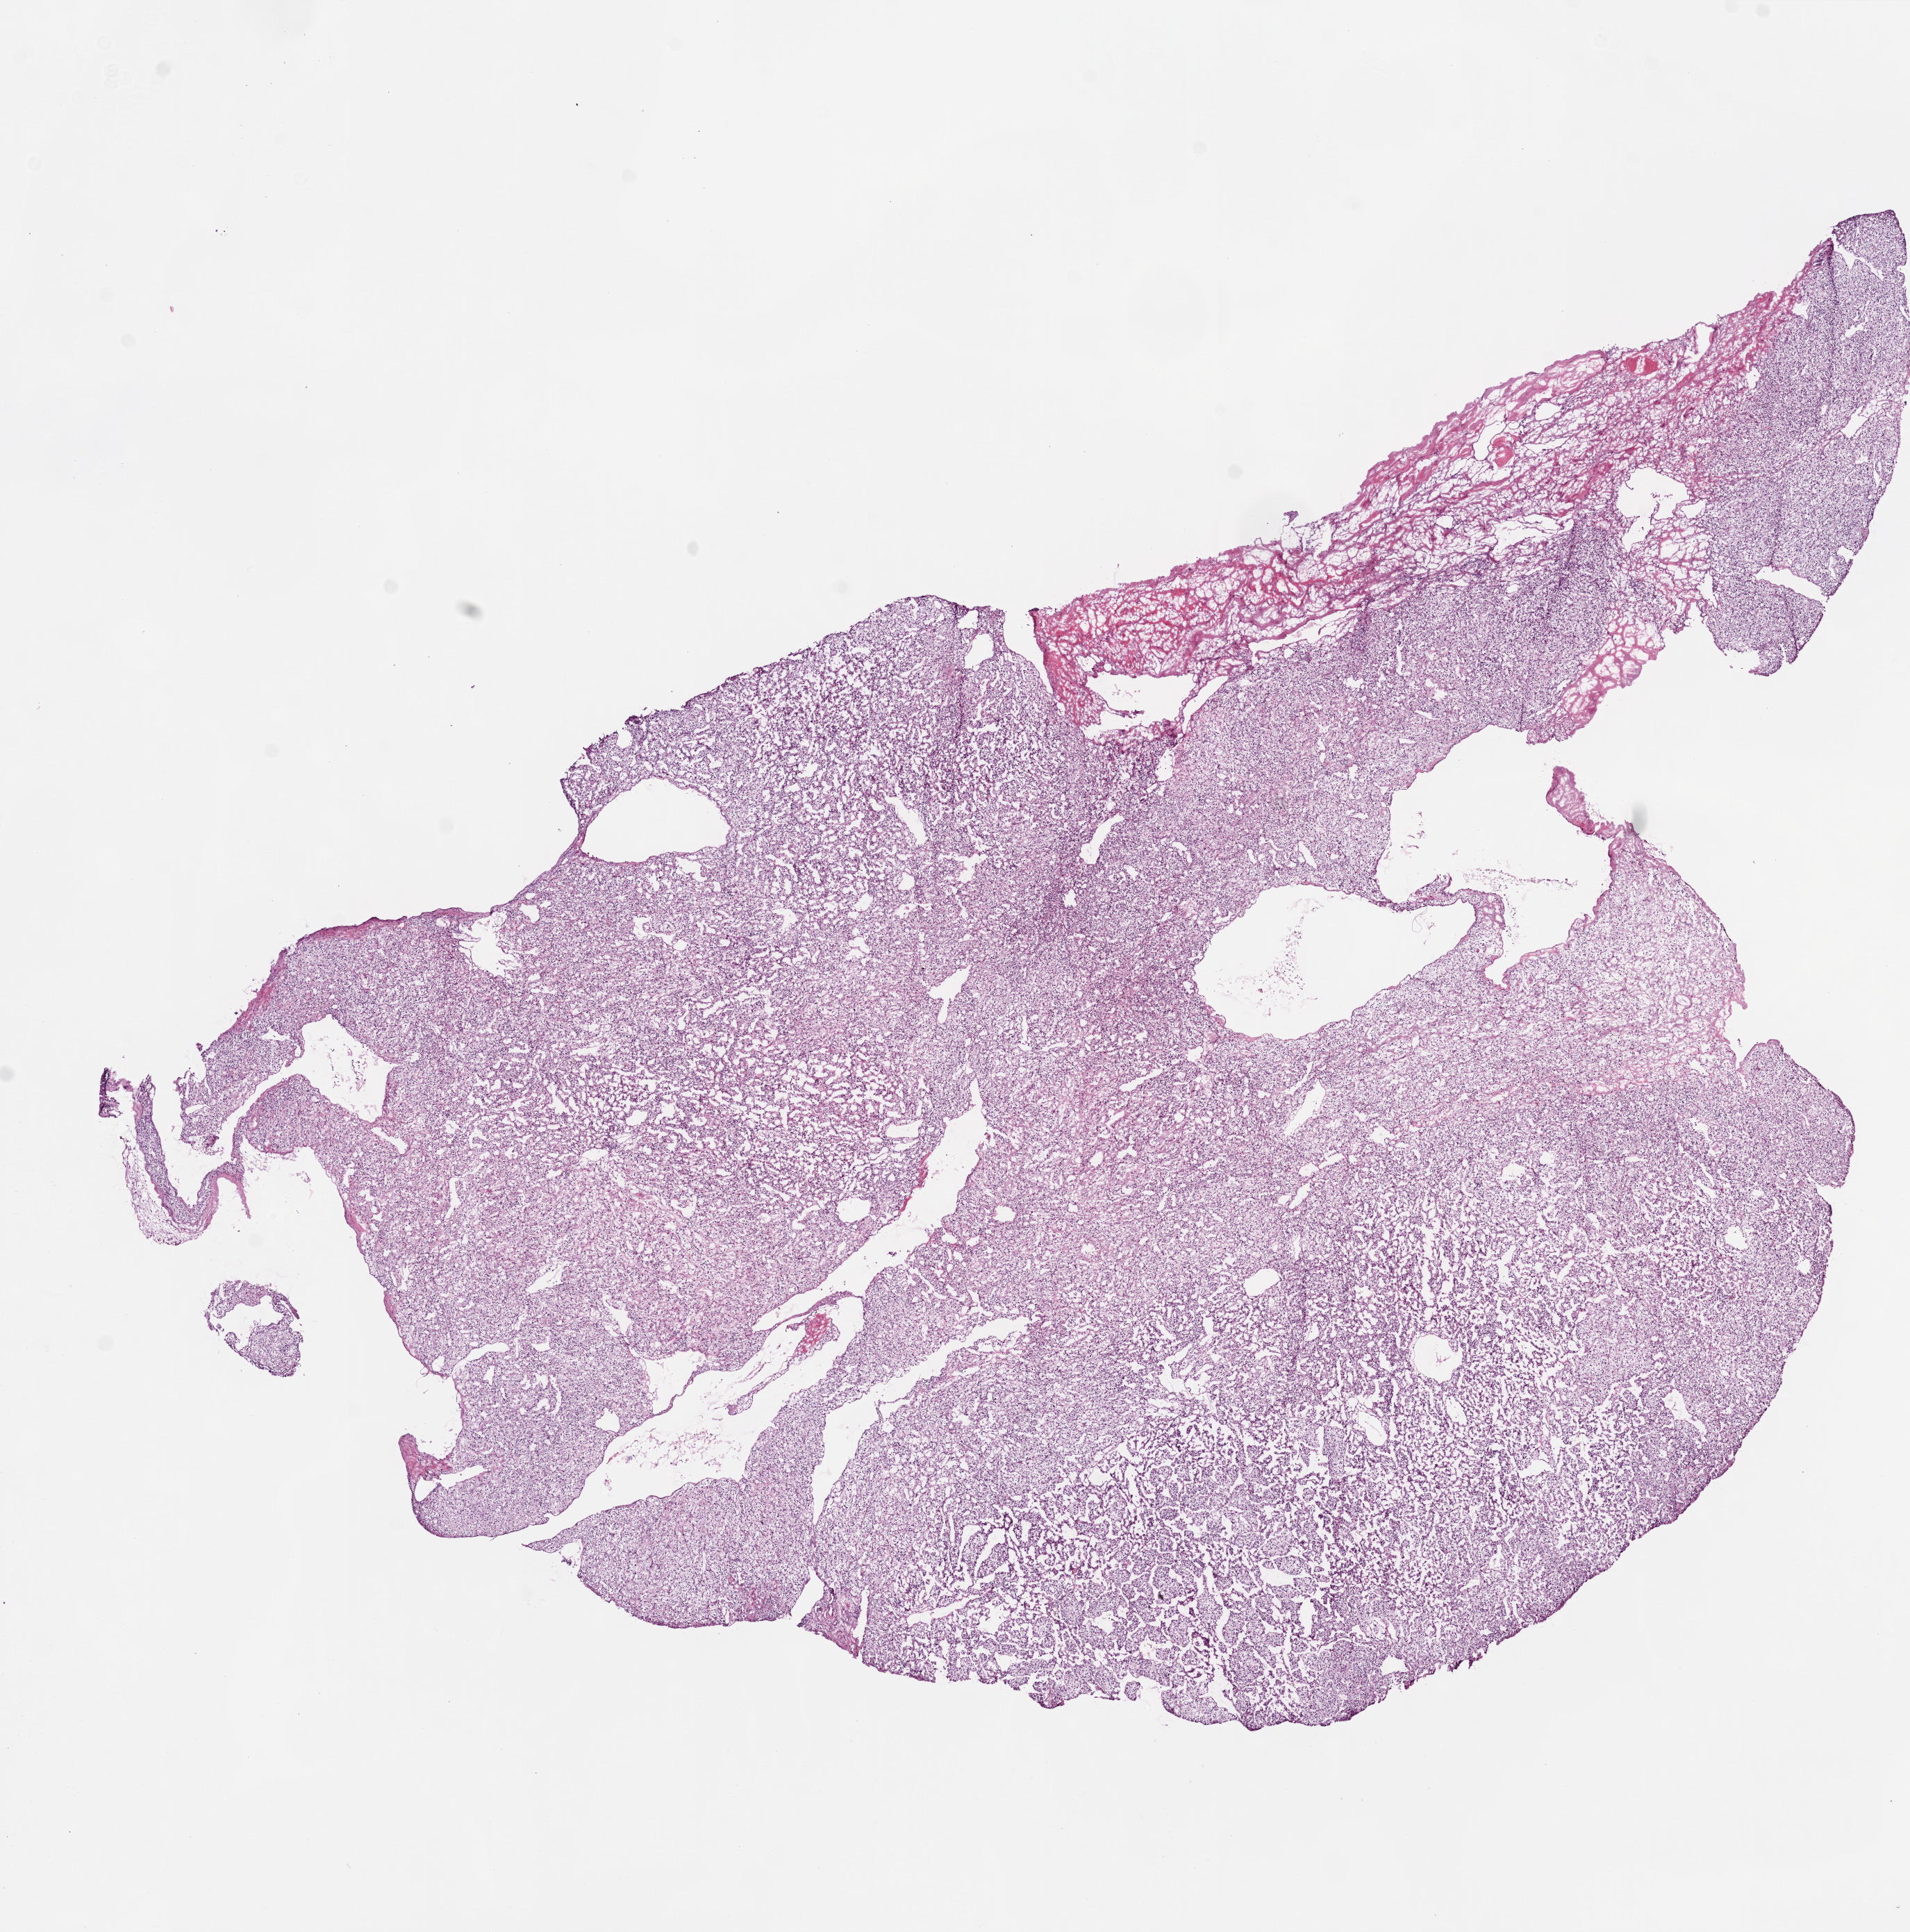
Whole-slide histology image, H&E-stained, a low-resolution overview of the entire scanned area, about 11.0 x 11.2 mm; frozen section; kidney, primary tumour sample. Patient sex: male. Histologic grade: G3 (poorly differentiated). Composition of this section per pathologist review: tumour cells 90%, tumour nuclei 90%, normal cells 0%, stromal cells 10%, necrosis 0%.
AJCC pathologic stage: II. Pathologic diagnosis: Clear cell adenocarcinoma, NOS.